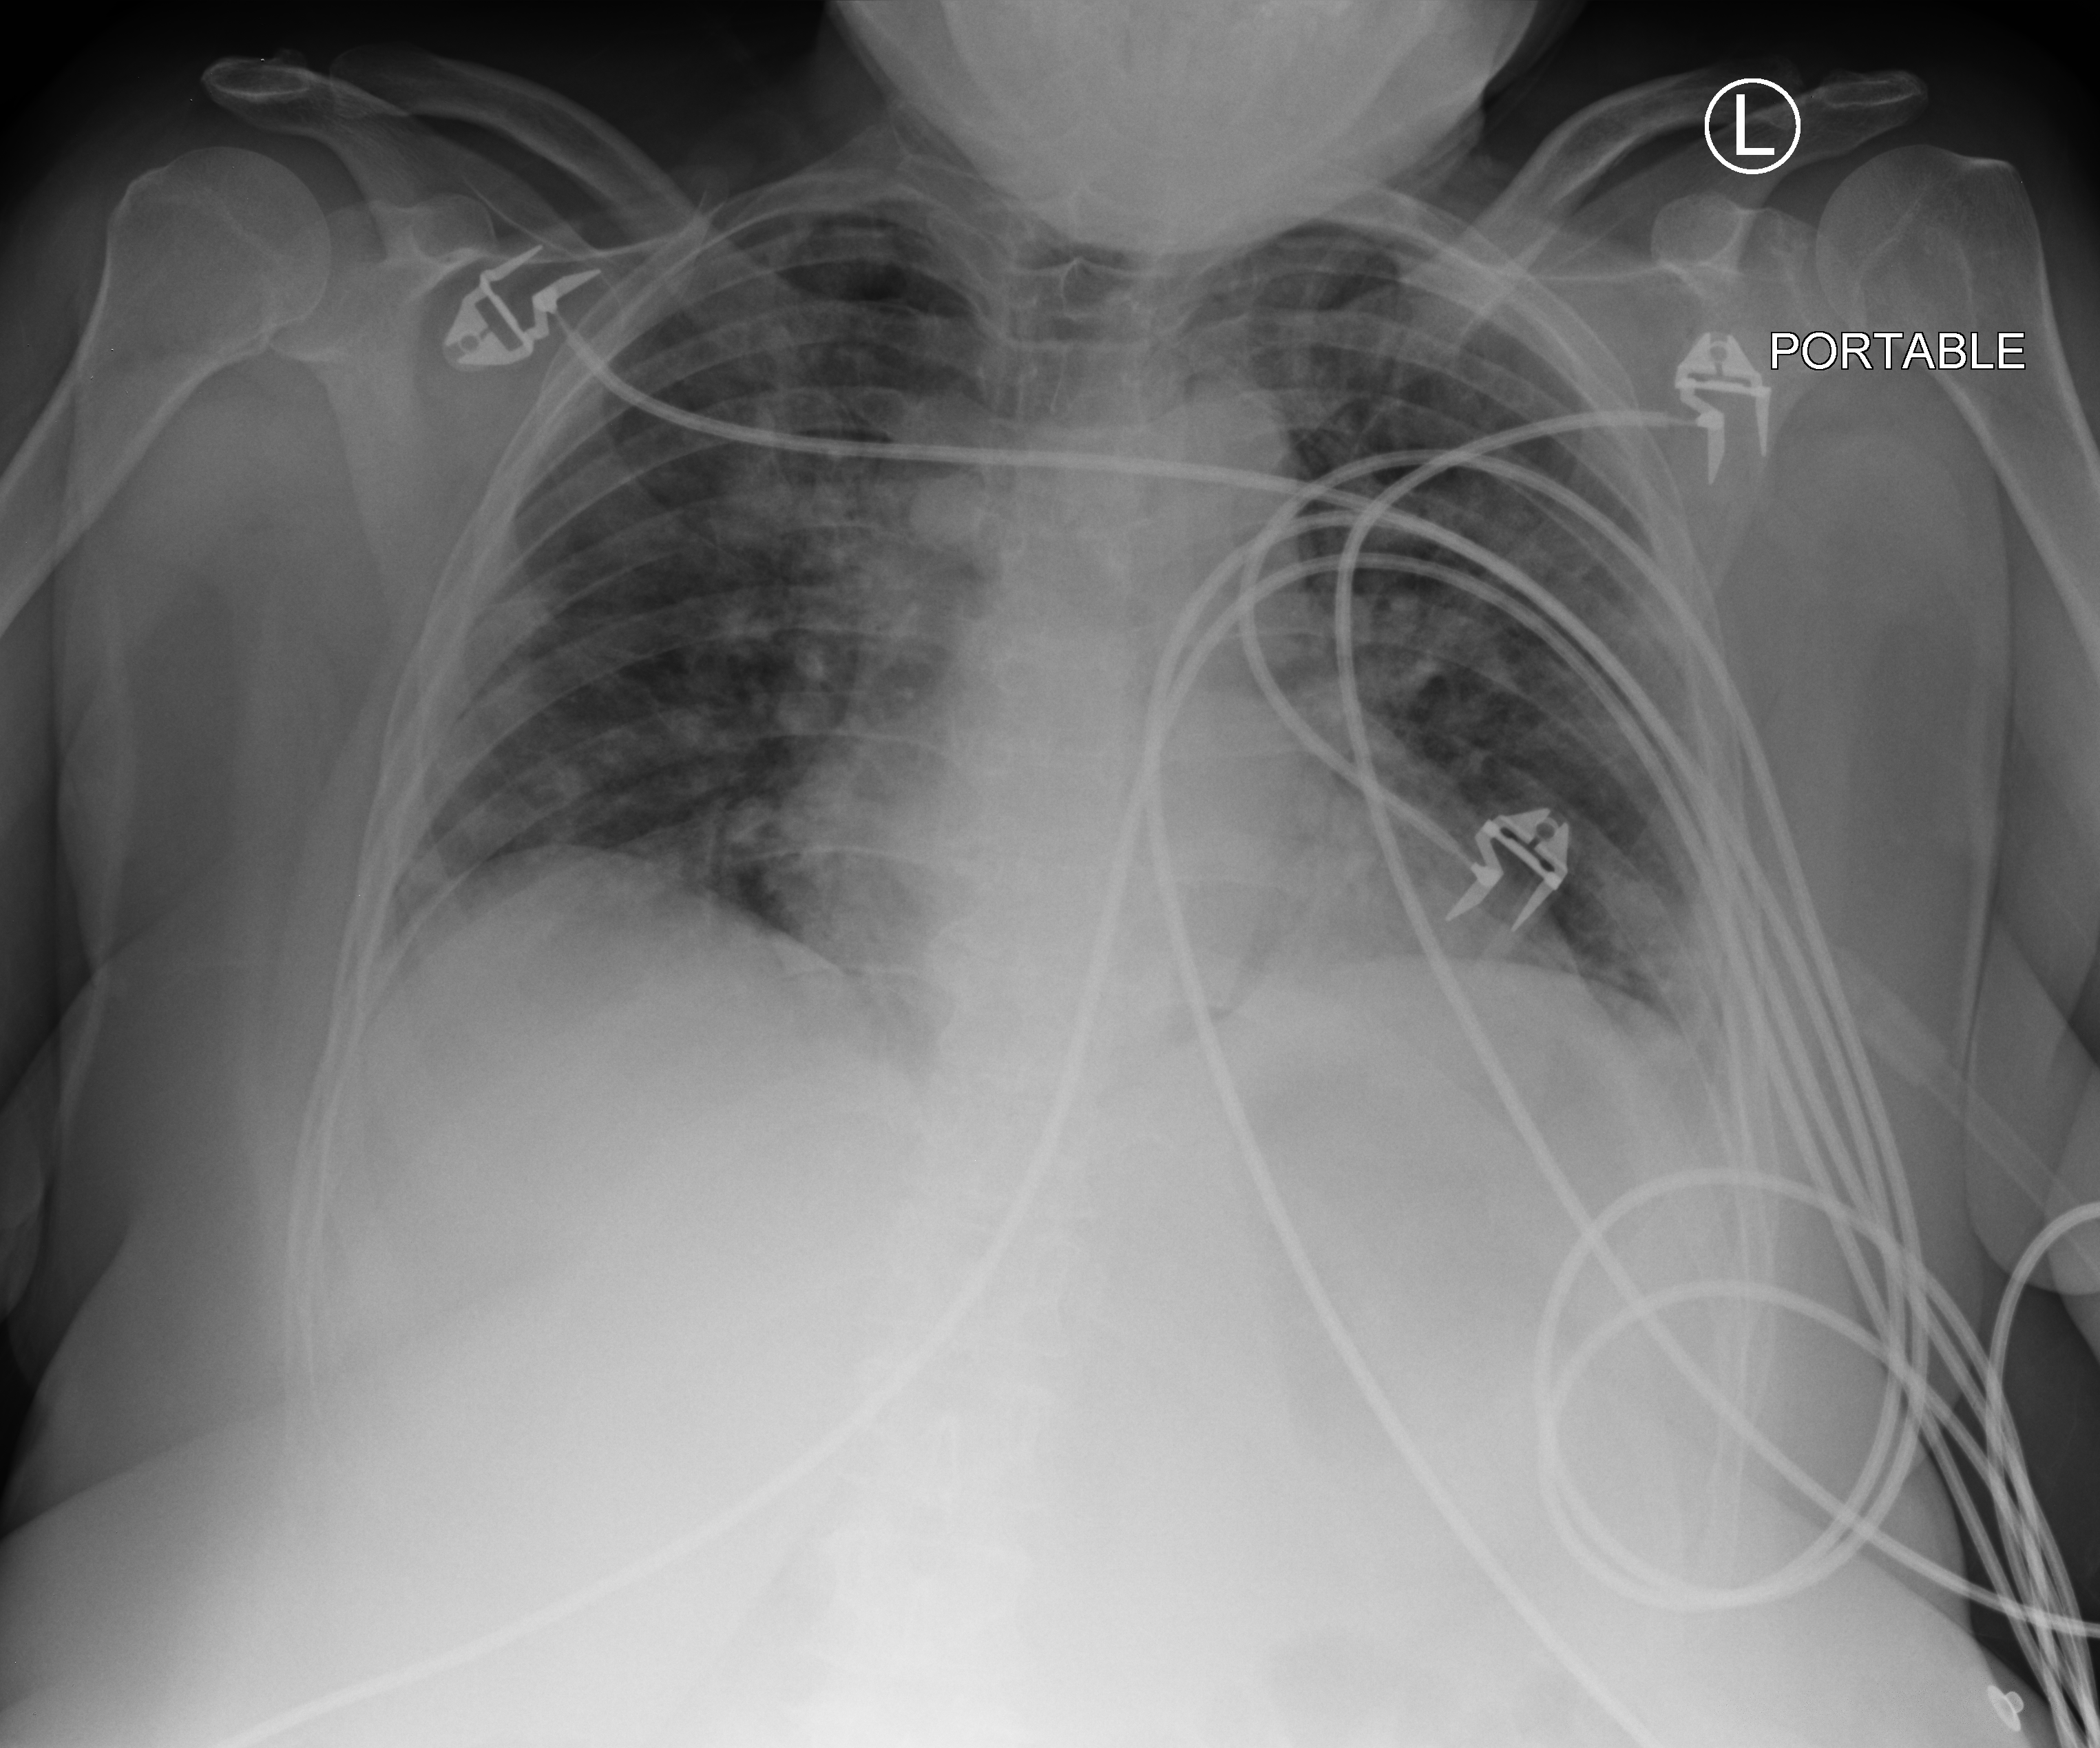
Portable chest radiograph. Patient hospitalised with COVID-19; female, aged 18–59 years.
From the hospital-stay record, not from the radiograph (when in the stay this image was taken is not recorded): smoking status (admission record): never; other chronic lung disease (admission record): yes.